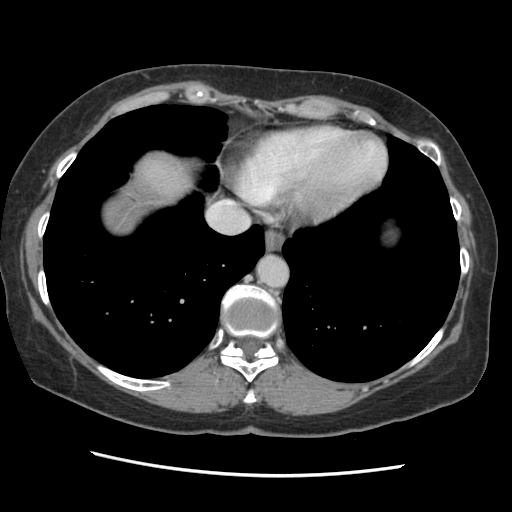
Contrast-enhanced abdominal CT, one axial slice; slice 126 of 141 in the series (ordered by position); 120 kVp; soft-tissue window (W 400 / L 40 HU); 2.5 mm slice thickness; 512 × 512 image matrix, field of view 330 × 330 mm. Female patient, age 61 years. From the clinical record (not read from this slice): diagnosis: colorectal cancer liver metastases, imaged before liver resection; multiple liver metastases: no; largest metastasis: 2.4 cm; disease in both lobes: no.
Structures marked on this image (outlined manually by an expert reader):
- liver: bounding box <106,150,200,219> (left, top, right, bottom; pixels)
- planned liver remnant (the part of the liver to remain after resection): <107,150,199,219>